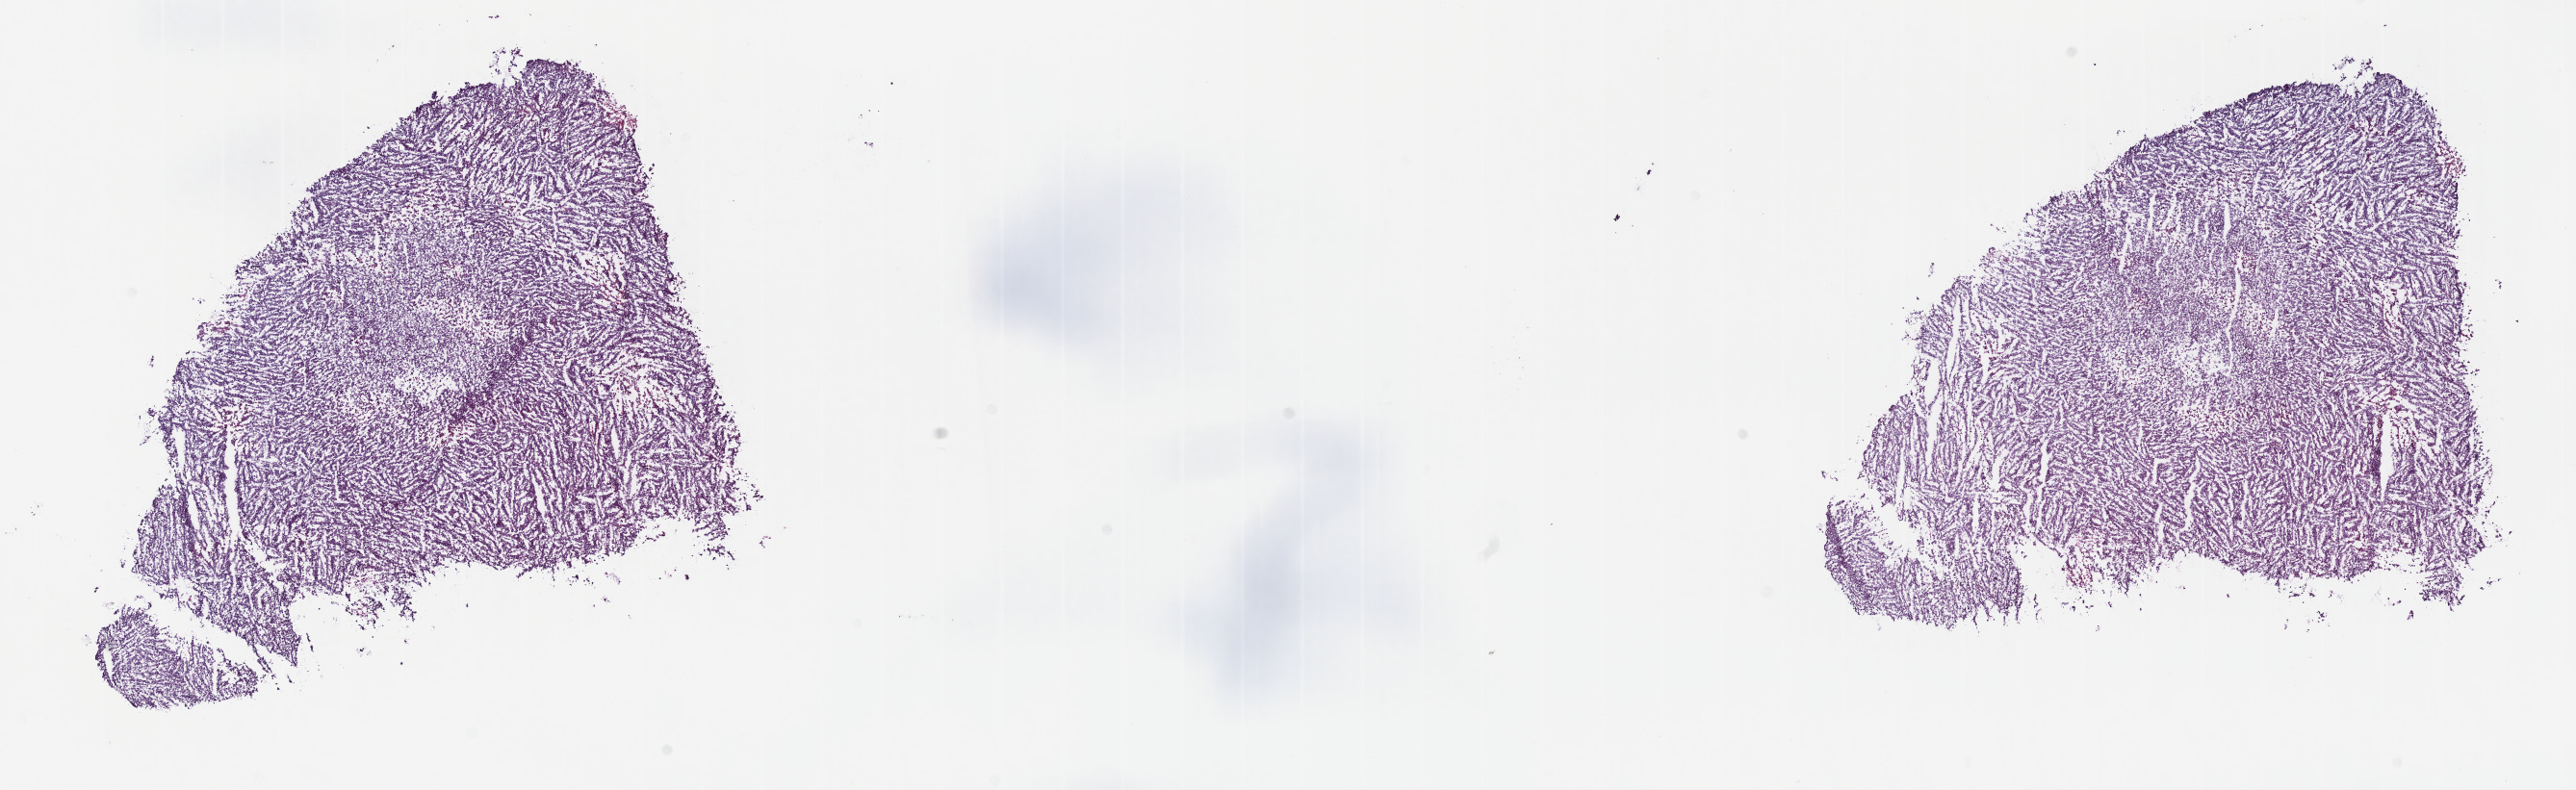
Whole-slide histology image, H&E-stained — a low-resolution overview of the entire scanned area, about 21.6 x 6.6 mm (acquisition: 40x scan); frozen section from the top of the tissue portion; primary tumour sample from the testis. Patient: male, age at initial diagnosis 45 years. Composition of this section per pathologist review: tumour cells 100%, tumour nuclei 80%, normal cells 0%, stromal cells 0%, necrosis 0%. Infiltration values recorded for this section: lymphocyte infiltration 2%, monocyte infiltration 0%, neutrophil infiltration 0%.
AJCC pathologic stage: IIIC (6th edition). Pathologic diagnosis: Seminoma, NOS.